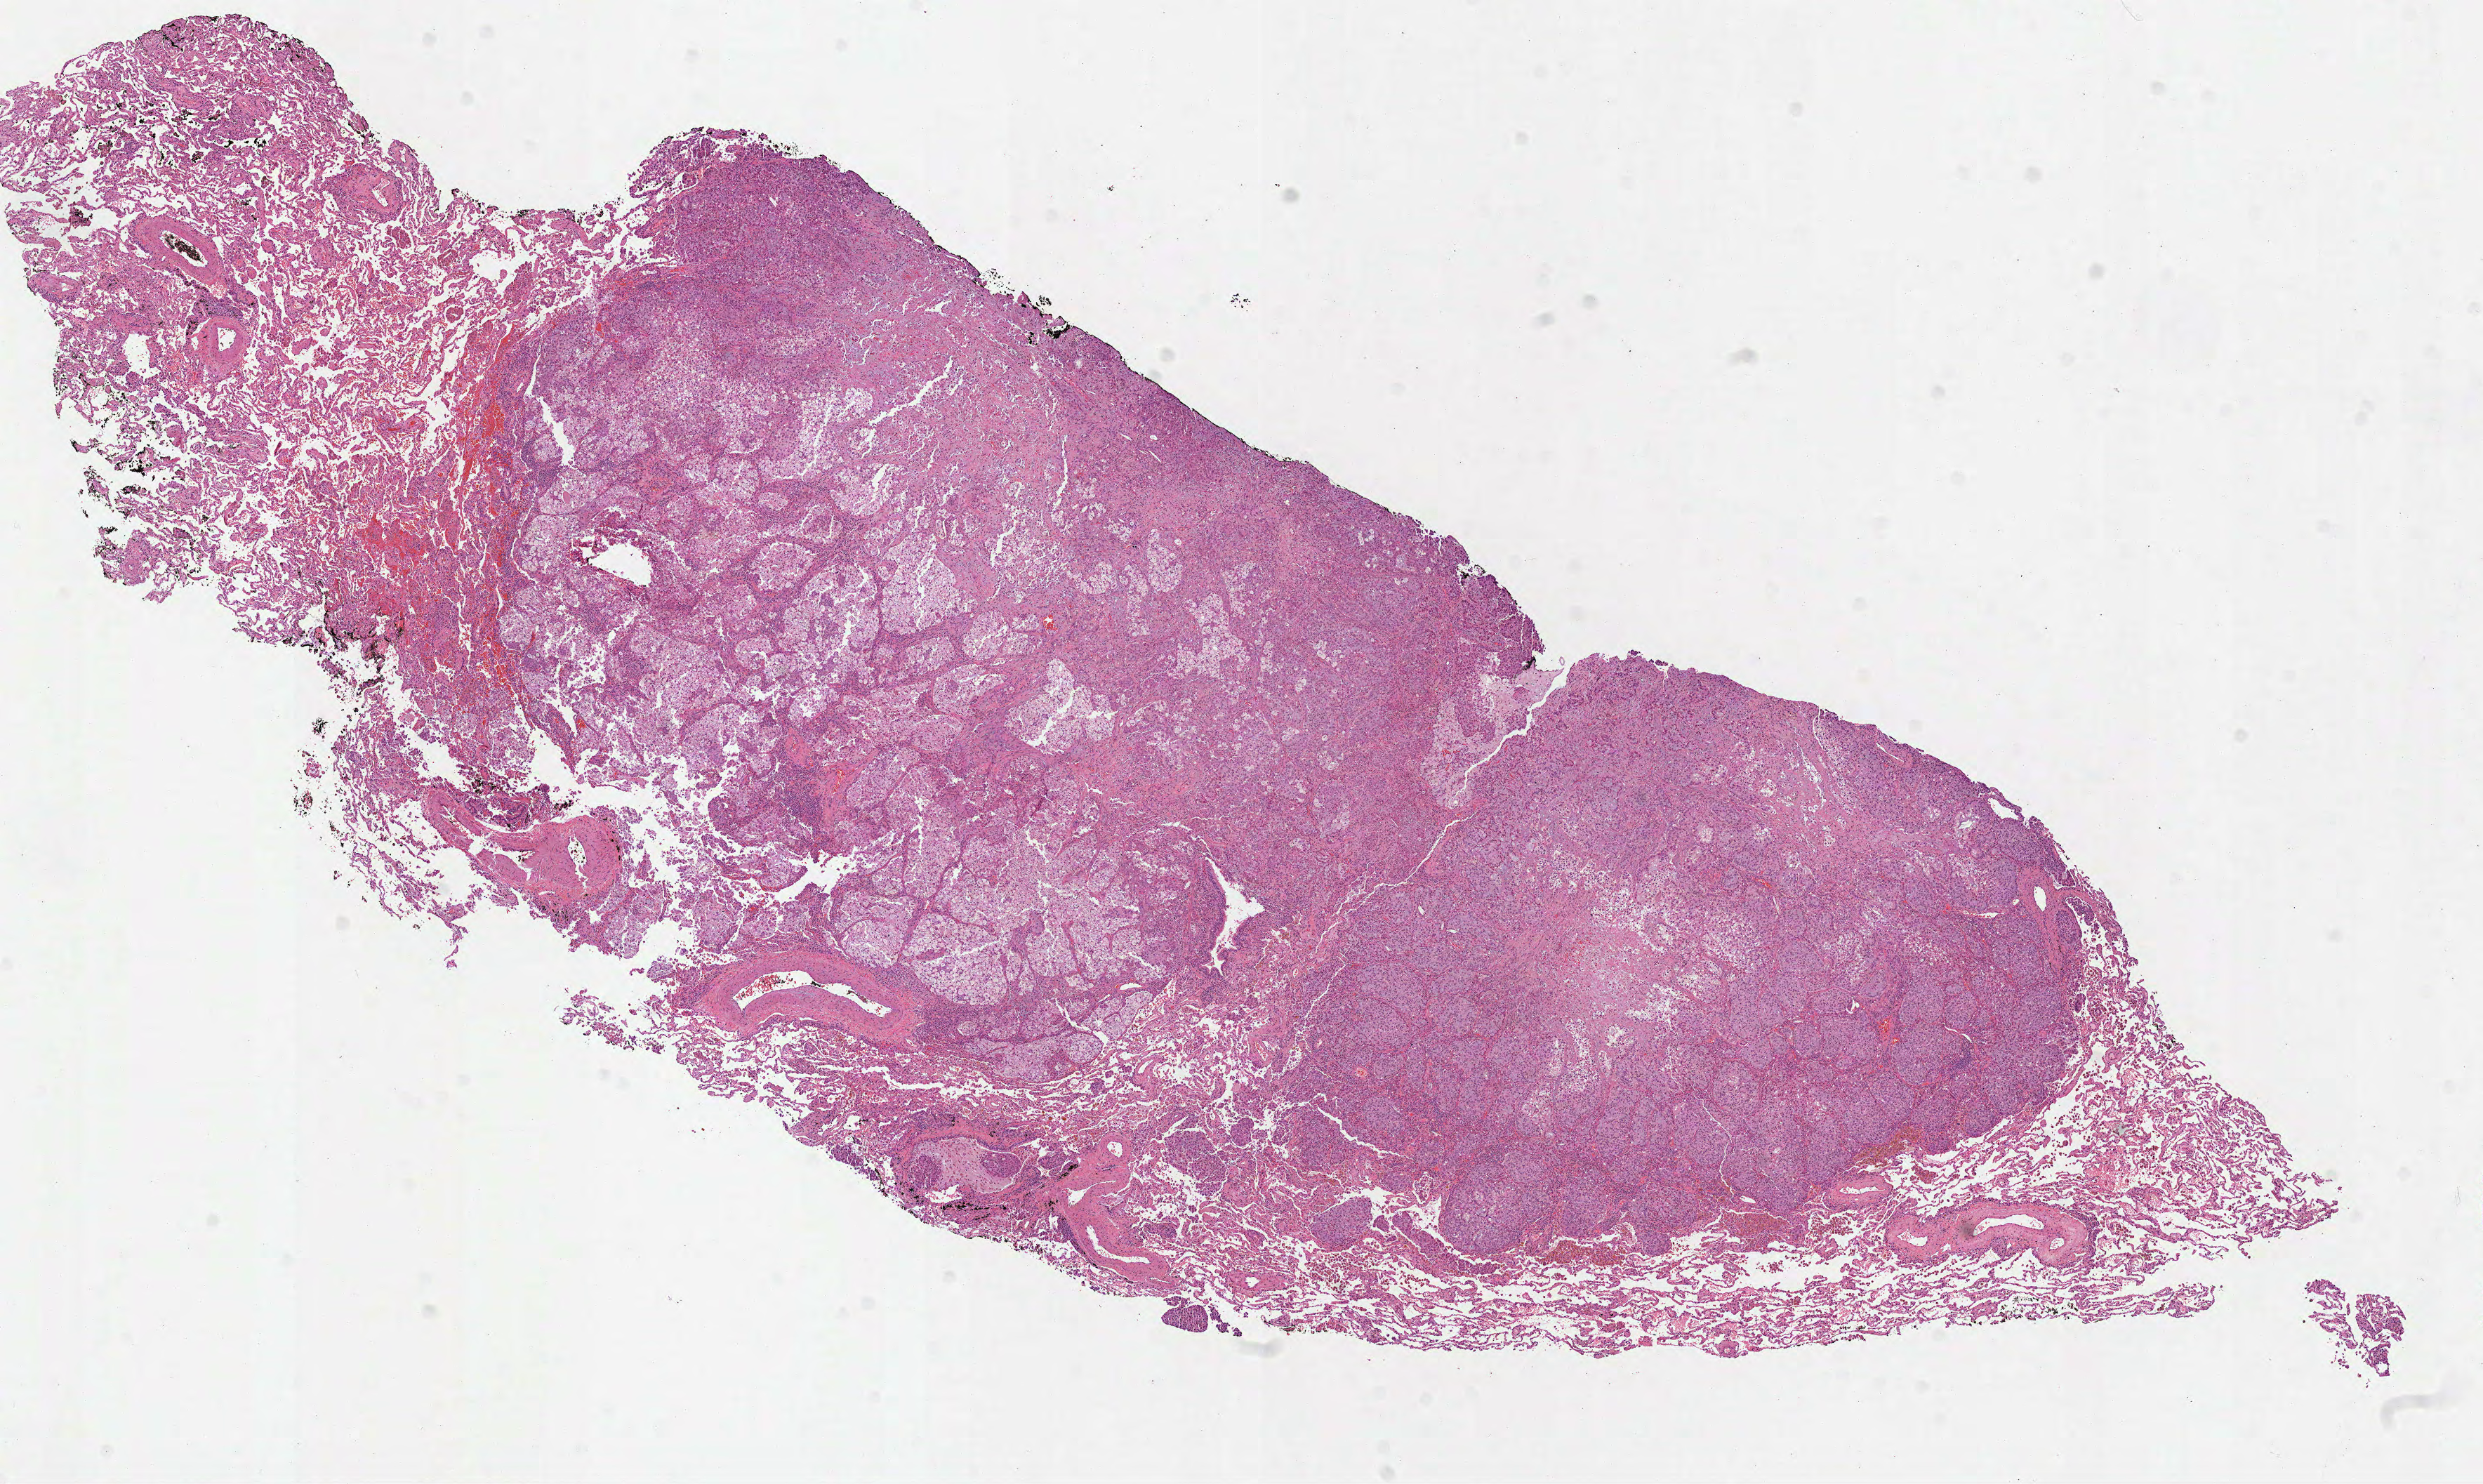
Hematoxylin and eosin (H&E) stained whole-slide image — whole scanned area (about 14.3 x 8.5 mm, from a 40x scan) shown as a low-resolution overview. FFPE section. Lung, primary tumour sample. Male, age 74 years at initial diagnosis.
AJCC pathologic stage: IB (7th edition). TNM: T2 N0 MX. Histologic diagnosis: Adenocarcinoma, NOS (lower lobe, lung).